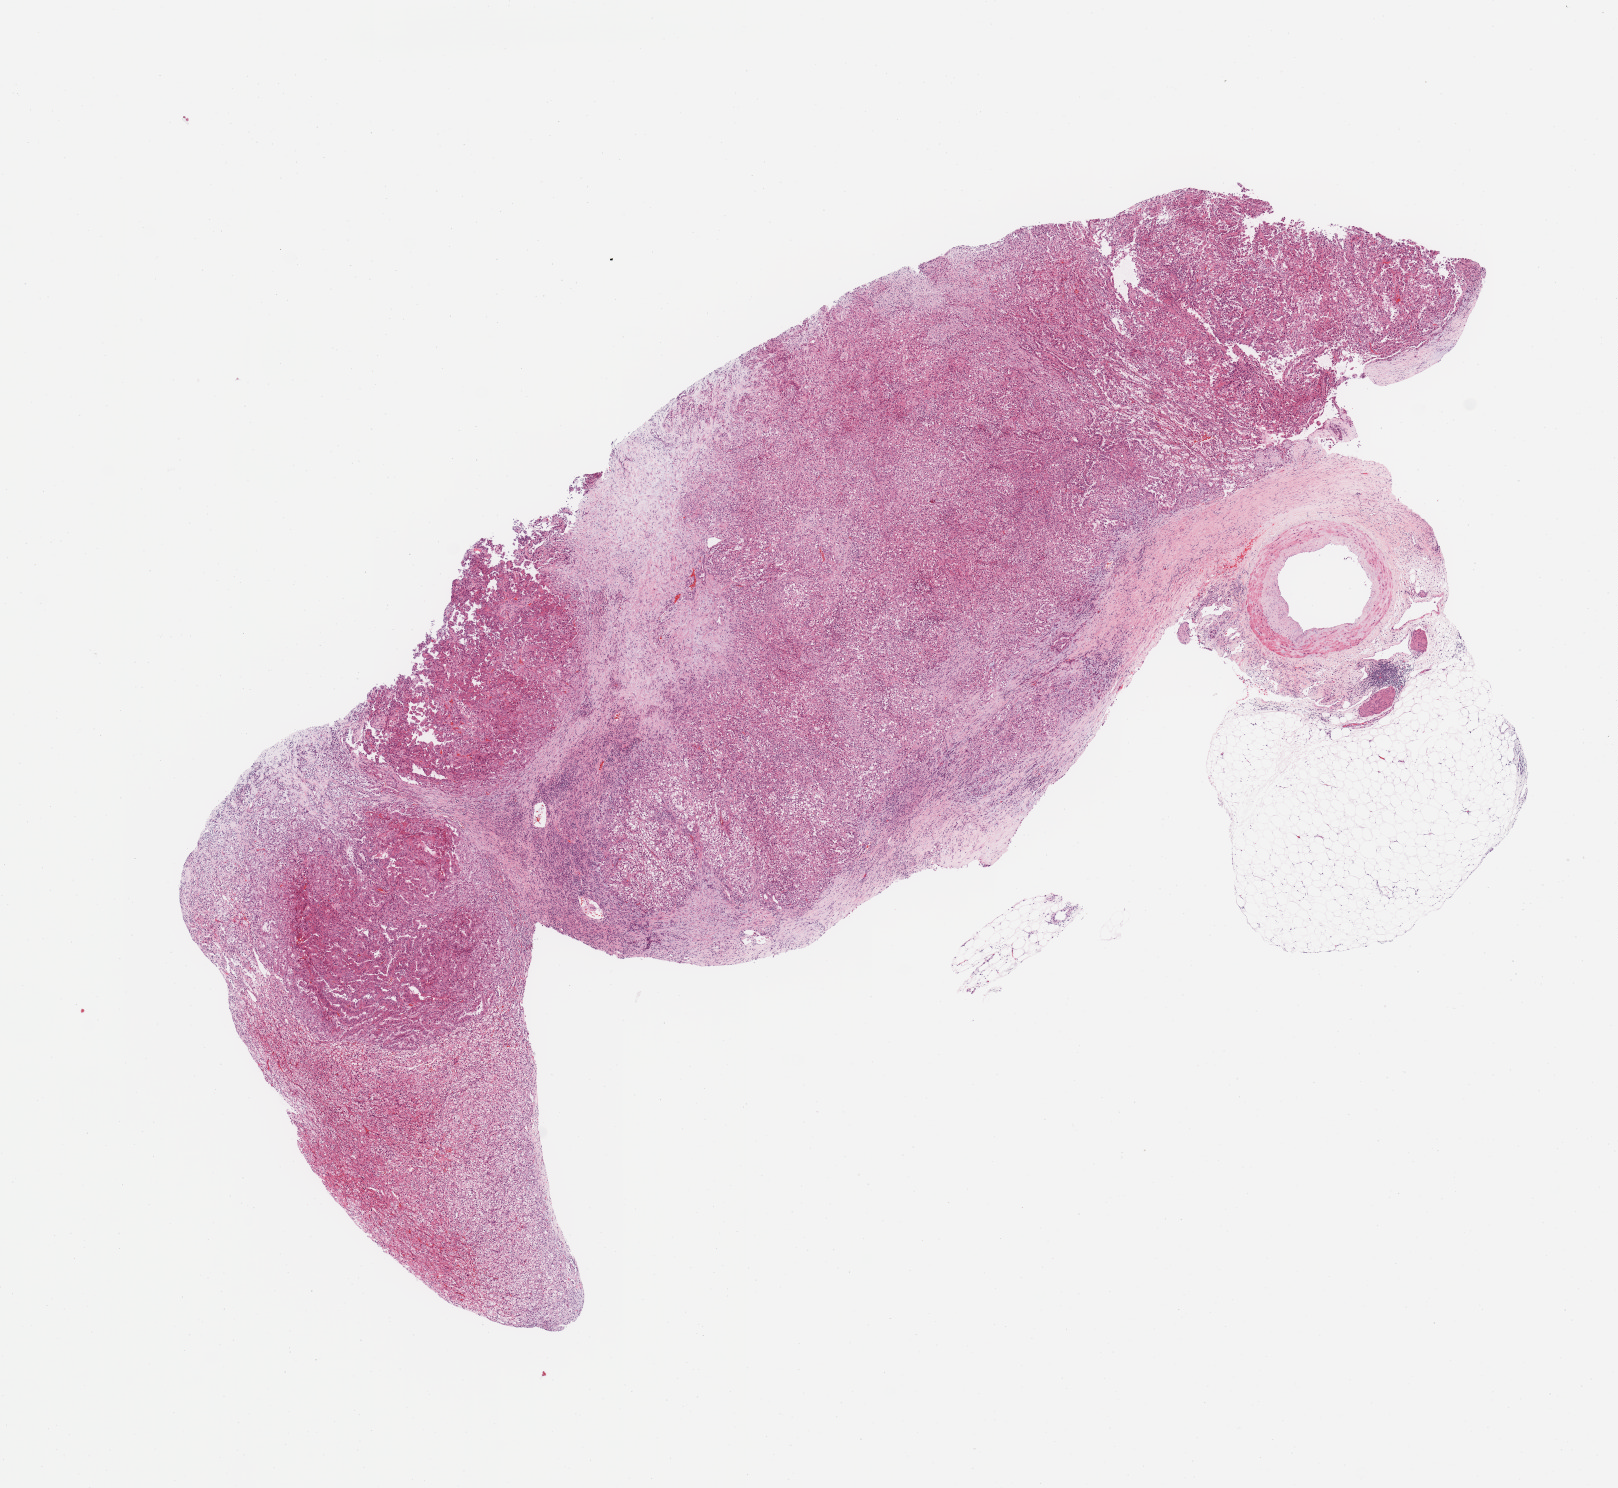
Whole-slide histology image, H&E — low-resolution overview of the scanned area, about 12.8 x 11.8 mm (from a 20x scan); tumour tissue sample, sampled site: kidney. 69-year-old male patient.
Histologic diagnosis: Renal cell carcinoma, NOS.